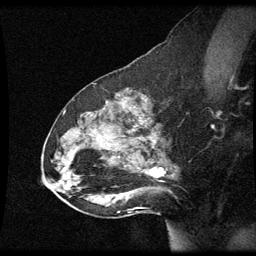
Breast MRI (dynamic contrast-enhanced), one sagittal slice; slice 35 of 60 in the series (ordered by position); dynamic contrast-enhanced series, image 2 of 3 at this slice position (ordered by acquisition); 1.5 T; TE 4.2 ms, TR 8.9 ms; 2 mm slice thickness; 256 × 256 image matrix. Patient: female, 49 years. From the clinical record (not read from this slice): setting: breast cancer imaged before/during neoadjuvant chemotherapy; receptor status: HR-positive, HER2-negative.
Annotated regions visible in this slice (semi-automatically segmented with operator editing):
- analysis volume of interest (the breast-tissue region the enhancement analysis was run in; not a lesion): box from (x=46, y=92) to (x=177, y=205) px
- tumour enhancement mask (voxels above the 70 % enhancement threshold inside the analysis volume of interest): (x=151, y=168)–(x=156, y=175)